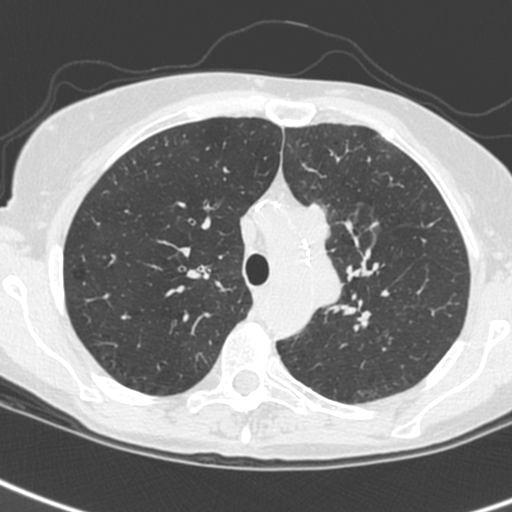
Low-dose screening chest CT, one axial slice; position 184 of 242 along the scan axis; lung window (W 1500 / L -600 HU); 1.3 mm slice thickness; 512 × 512 image matrix.
Annotated regions visible in this slice (outlined manually by an expert reader):
- lesion 3 (tumor, upper lobe of left lung): bounding box (x1, y1, x2, y2) in pixels: (298, 203, 342, 308)